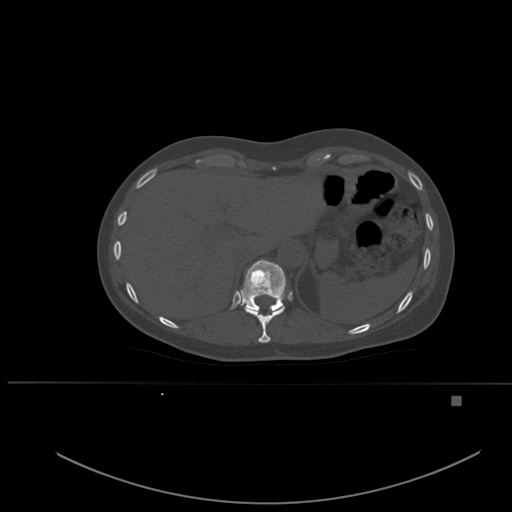
CT including the spine, one axial slice. Position 280 of 651 along the scan axis. Bone window (W 1800 / L 400 HU). 1.5 mm slice thickness. 512 × 512 image matrix. Female patient, age 49 years. From the clinical record (not read from this slice): primary cancer: breast.
Annotated regions visible in this slice (semi-automatic segmentation, software-assisted and operator-edited):
- T10 vertebra: bounding box [x1, y1, x2, y2] px = [245, 305, 285, 343]
- T11 vertebra: [240, 259, 286, 313]